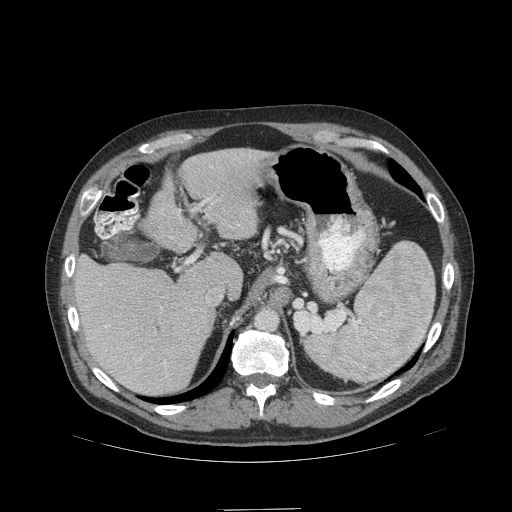
Contrast-enhanced abdominal CT (liver protocol), one axial slice; slice 72 of 99 in the series (ordered by position); 140 kVp; soft-tissue window (W 400 / L 40 HU); 2.5 mm slice thickness; 512 × 512 image matrix. From the clinical record (not read from this slice): diagnosis: hepatocellular carcinoma (patient treated with transarterial chemoembolisation; whether this scan precedes or follows treatment is not stated here); TNM stage (as recorded): Stage-I; Child-Pugh class: A; tumour differentiation: no biopsy.
Structures marked on this image (semi-automatic segmentation, software-assisted and operator-edited):
- liver parenchyma outside the tumour (the mass and vessels are separate outlines, so this box may not span the whole liver): bounding box <72,148,273,394> (left, top, right, bottom; pixels)
- liver vessels: <85,166,221,365>